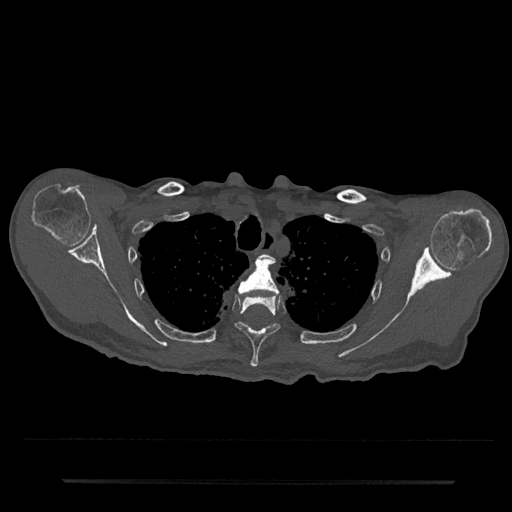
CT including the spine, one axial slice; position 626 of 797 along the scan axis; reconstruction kernel Br40s/3; bone window (W 1800 / L 400 HU); 512 × 512 image matrix, field of view 427 × 427 mm. Male patient, age 74 years. Case-level facts recorded for this patient, not image findings: primary cancer: prostate.
Outlined on this slice (semi-automatically segmented with operator editing):
- T2 vertebra: box from (x=263, y=254) to (x=269, y=259) px
- T3 vertebra: (x=237, y=256)–(x=279, y=296)
- T4 vertebra: (x=235, y=295)–(x=280, y=367)